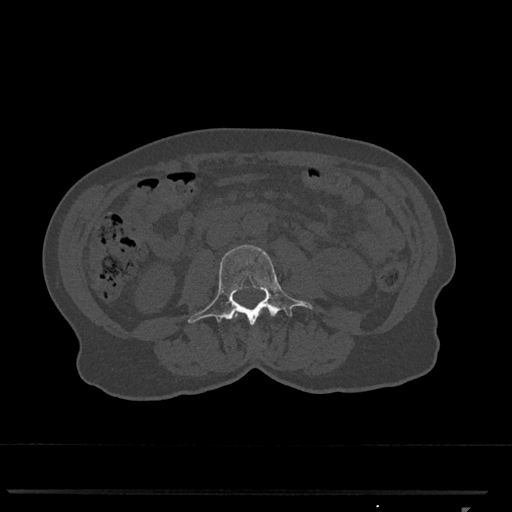
CT including the spine, one axial slice; slice 280 of 793 in the series (ordered by position); reconstruction kernel Br40s/3; 120 kVp; bone window (W 1800 / L 400 HU); 512 × 512 image matrix, field of view 380 × 380 mm. Patient: female, 62 years. Case-level facts recorded for this patient, not image findings: primary cancer: renal.
Outlined on this slice (semi-automatically segmented with operator editing):
- L2 vertebra: bounding box [x1, y1, x2, y2] px = [234, 314, 237, 317]
- L3 vertebra: [188, 245, 313, 326]